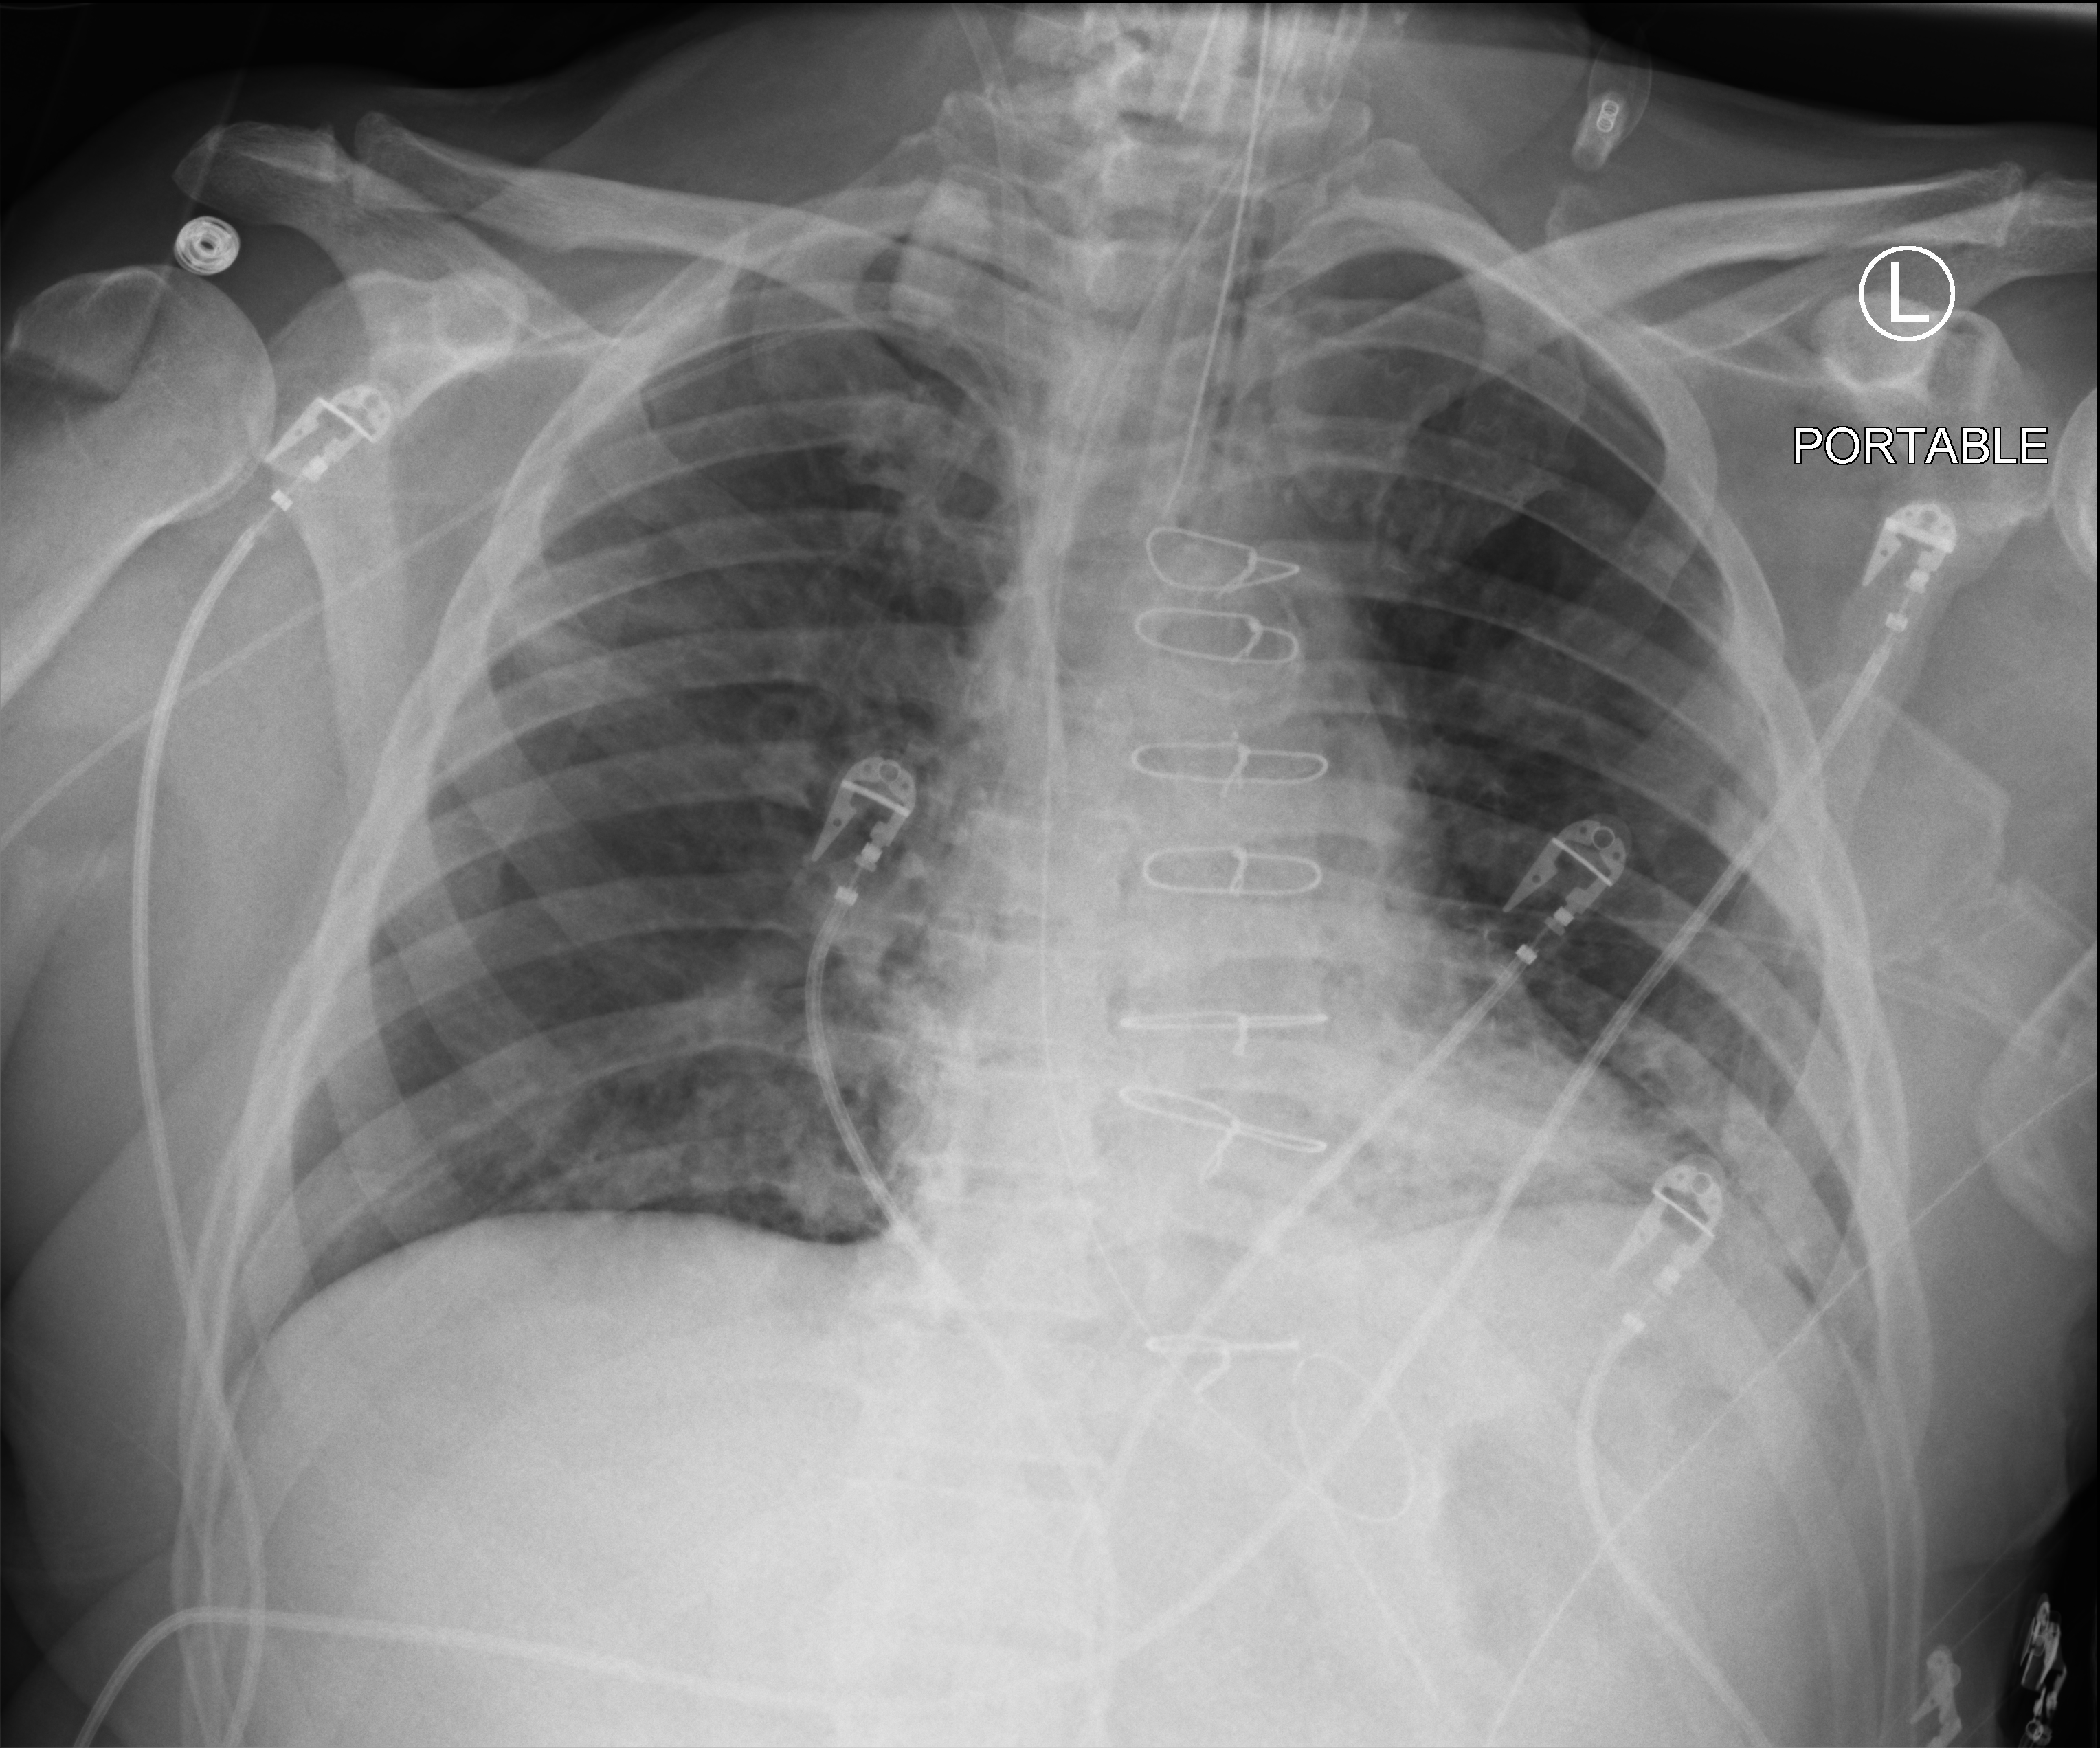
Portable chest radiograph, anteroposterior (AP) projection. Patient hospitalised with COVID-19; male, aged 60–74 years.
Admission-level facts for this patient (not findings on this image; timing relative to this image not recorded): smoking status (admission record): former.